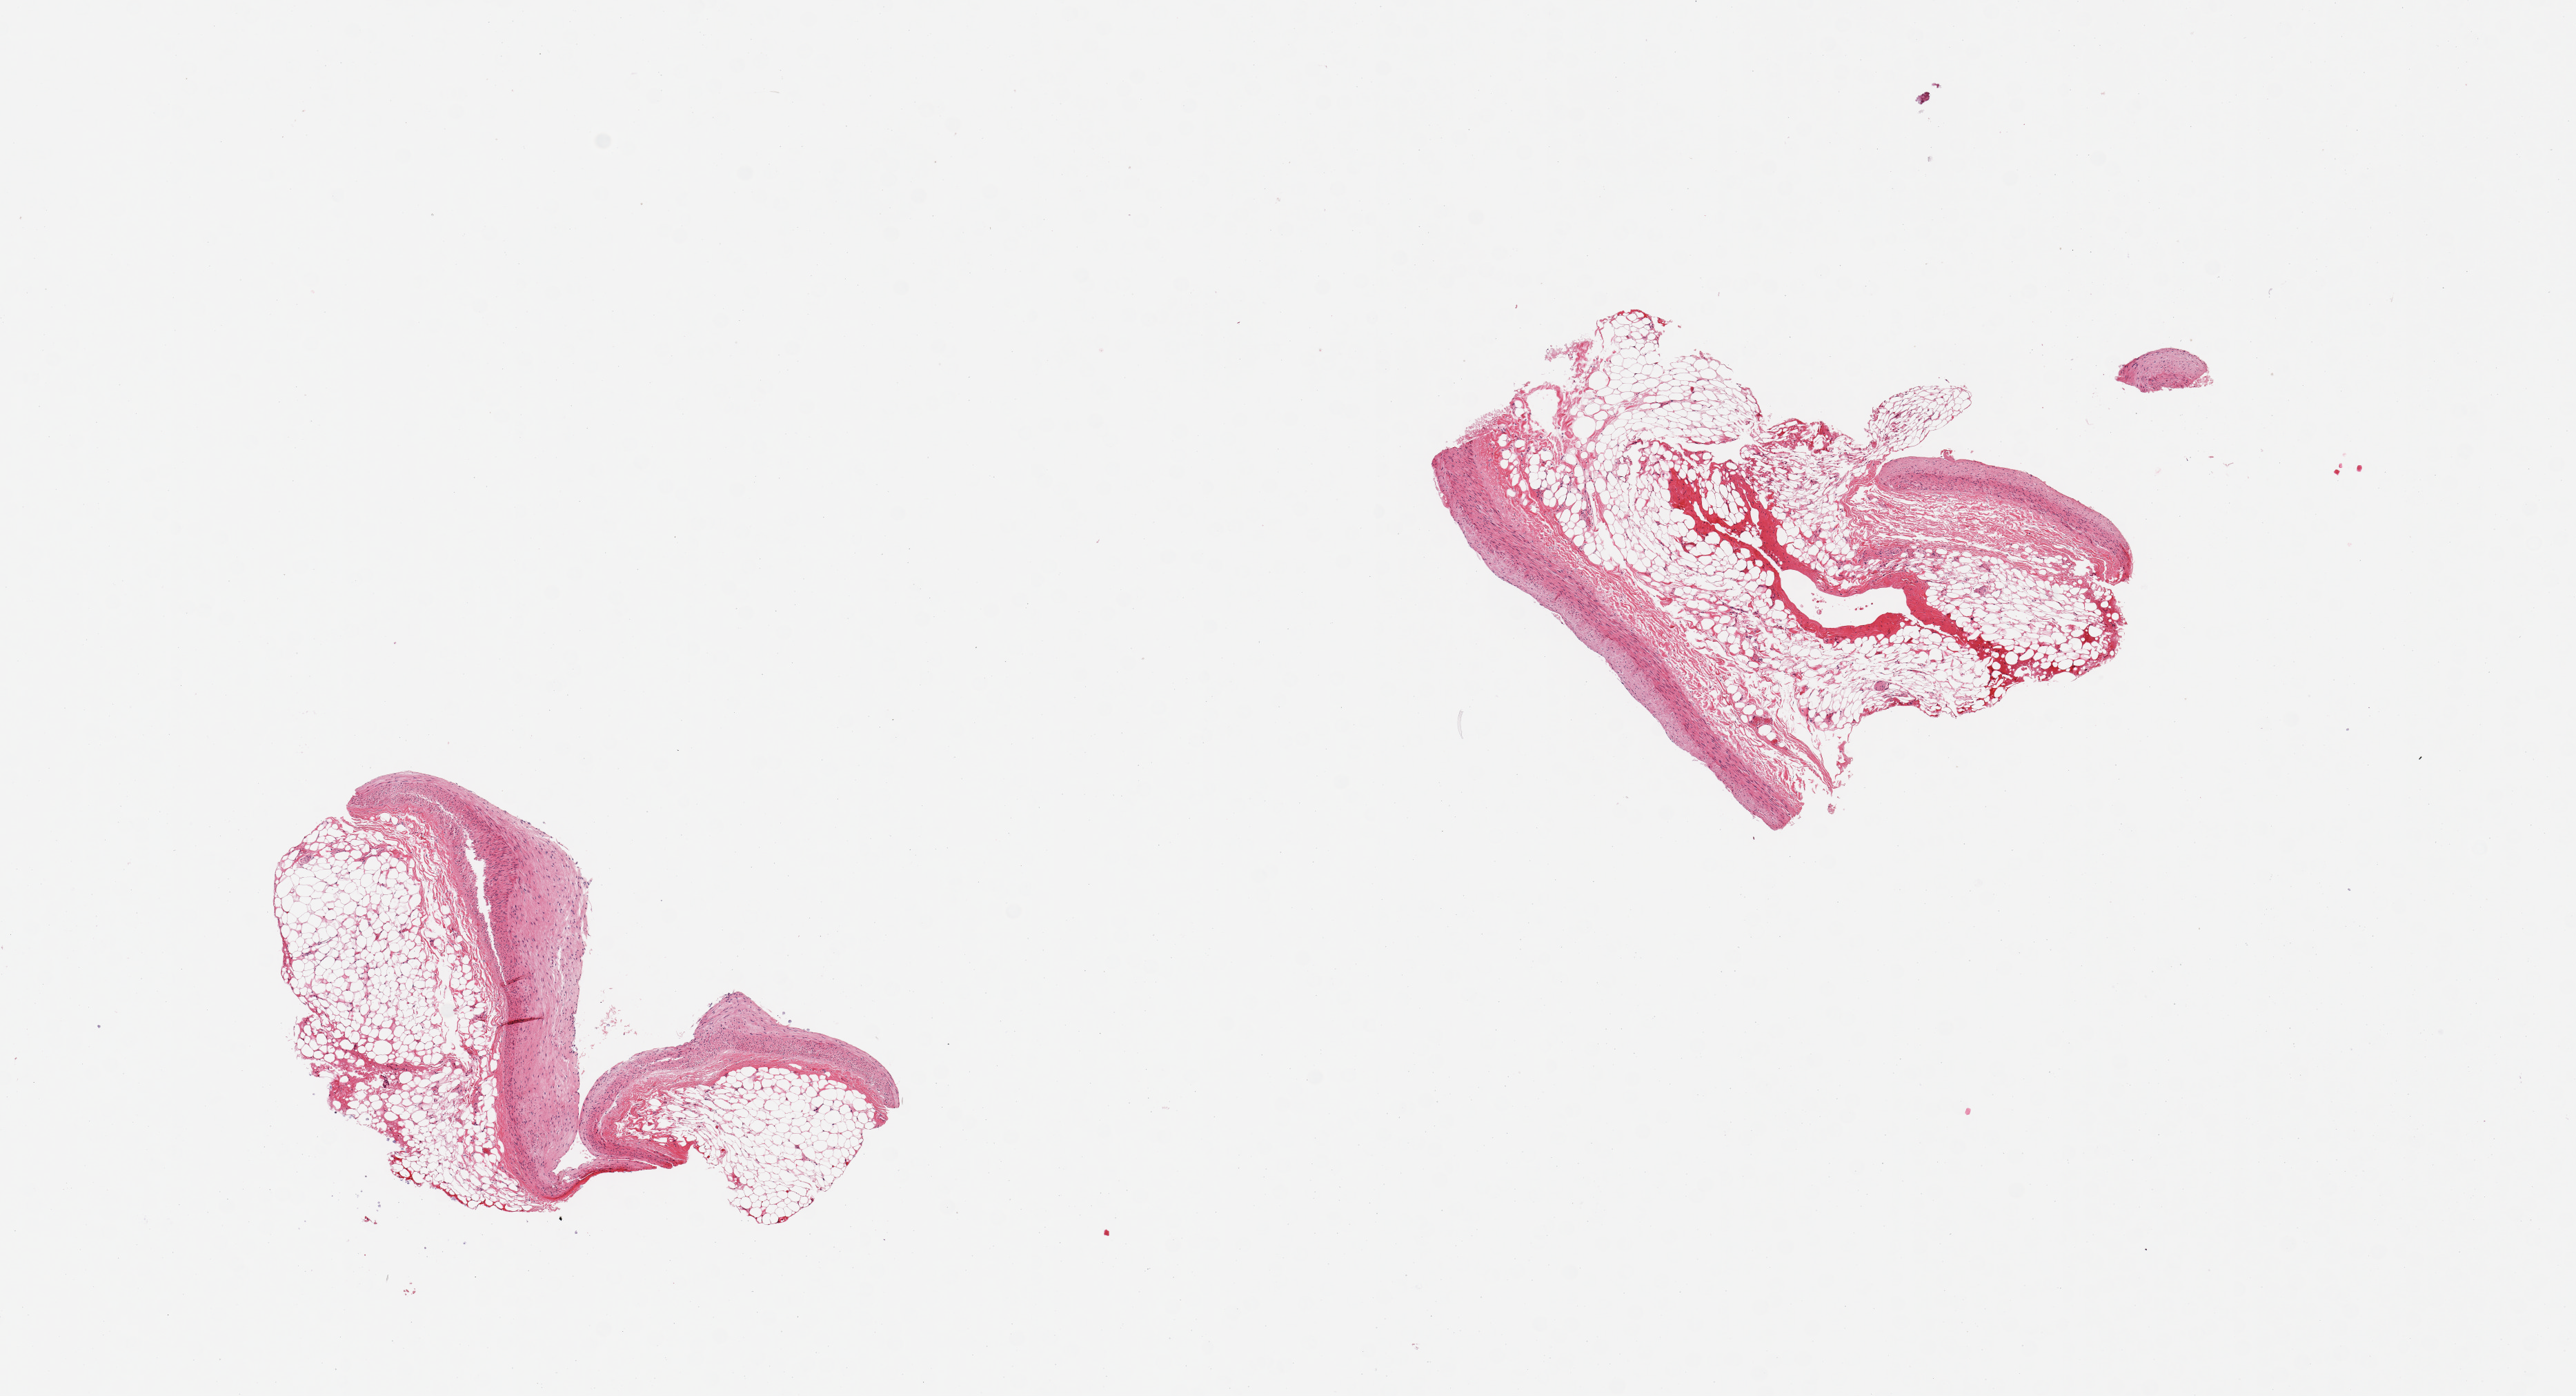
Hematoxylin and eosin (H&E) whole-slide image, whole scanned area (about 14.8 x 8.0 mm, acquisition: 20x scan) shown as a low-resolution overview, PAXgene-fixed paraffin-embedded (PFPE) section, section of coronary artery (target tissue), tissue donor sample. Donor sex: male.
Pathologist's review note for this sample: 2 pieces; poorly oriented specimen consists of adipose tissue and fragmented vascular wall with possible fibrous plaque.